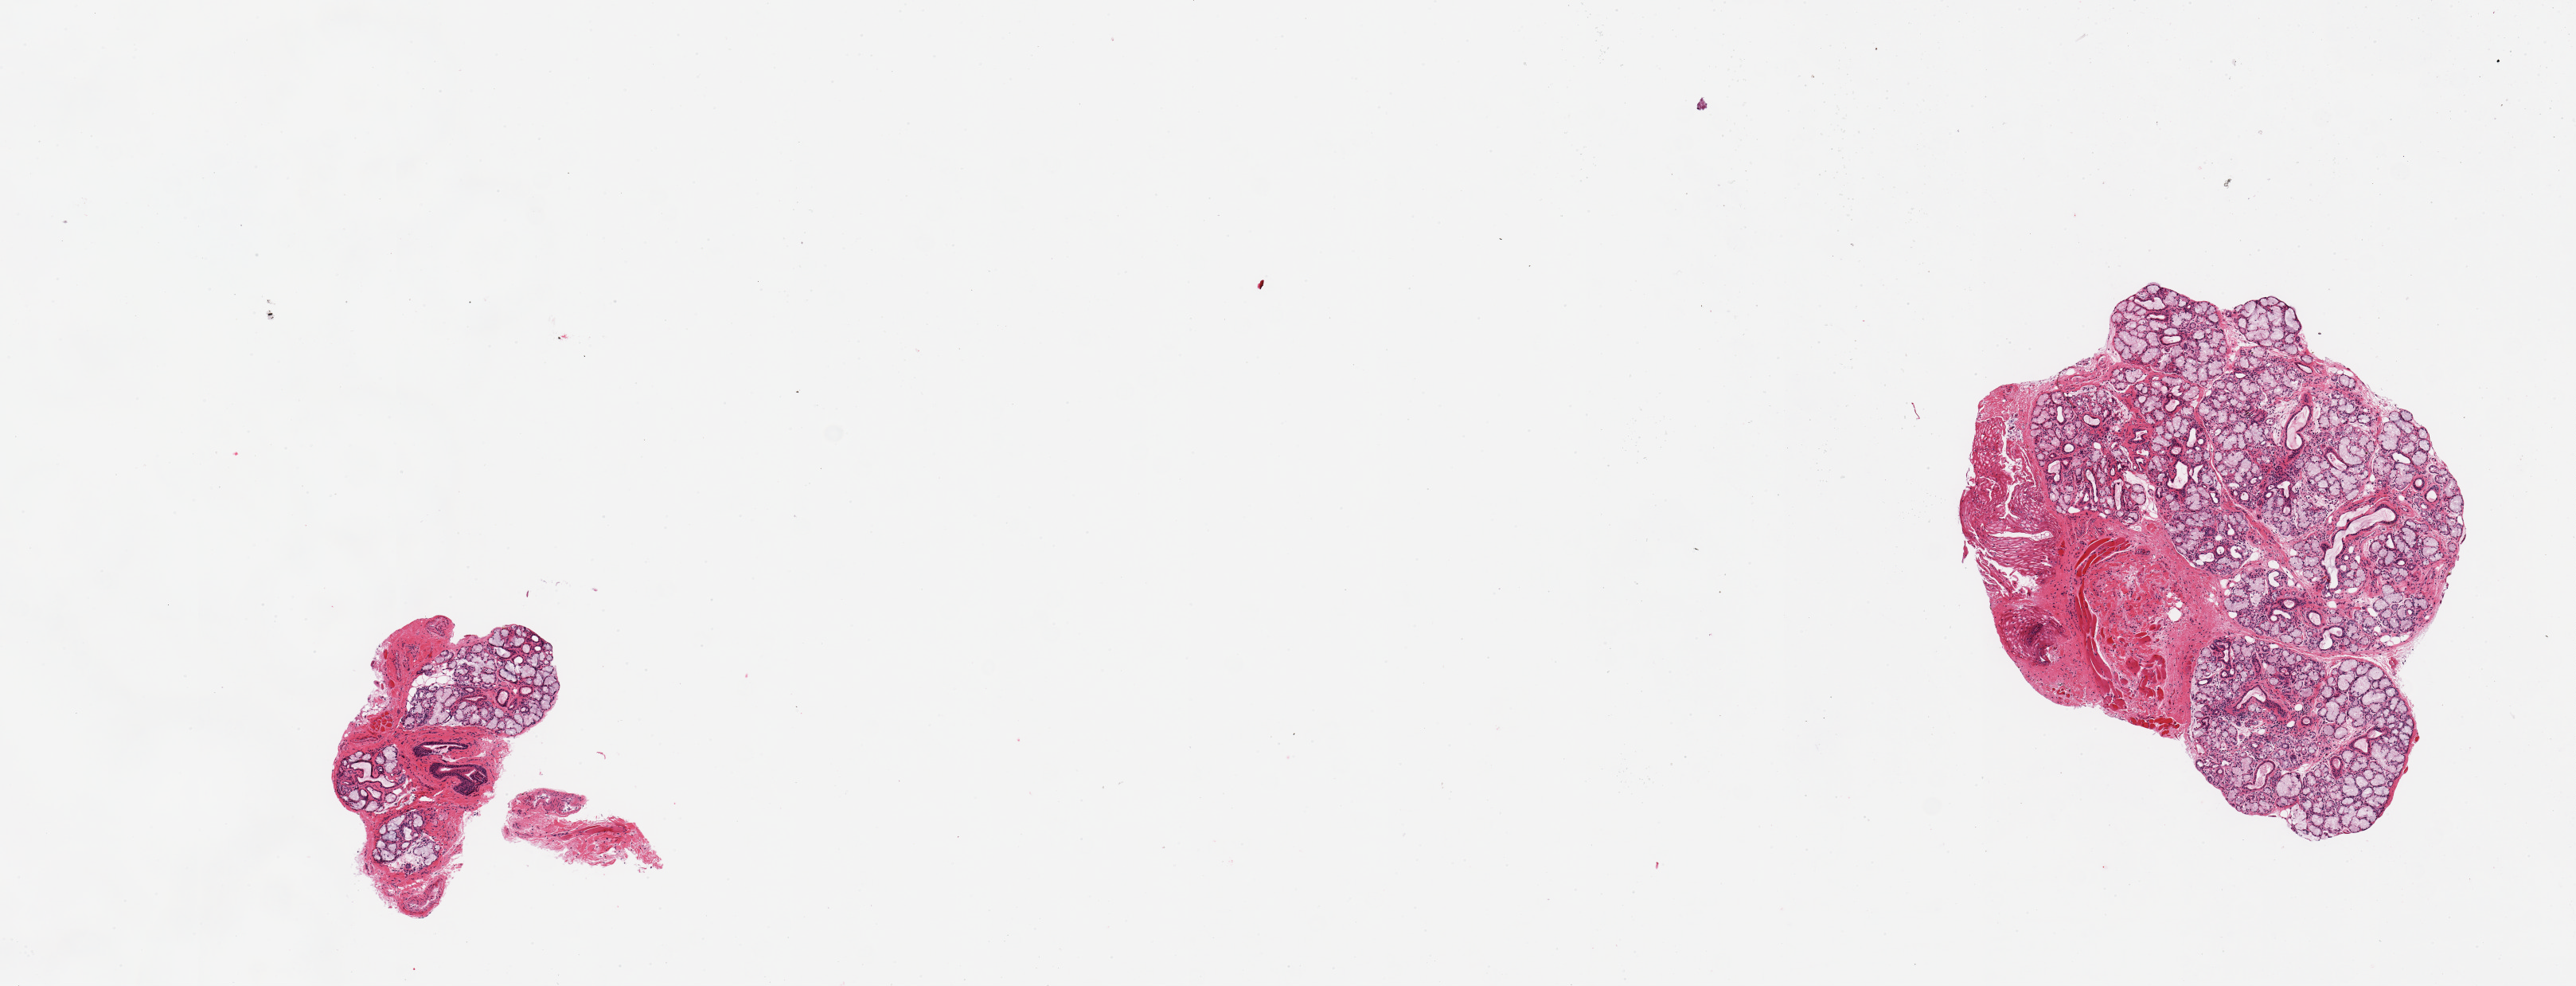
Whole-slide image, haematoxylin and eosin stain — low-resolution overview of the scanned area, about 12.8 x 4.9 mm. PAXgene-fixed, paraffin-embedded tissue. Target tissue: minor salivary gland. Tissue donor sample. Male donor.
Review note (as recorded): 2 pieces, glandular elements are ~70% of tissue, rest is fibroconnective, skeletal muscle, squamous epithelium.